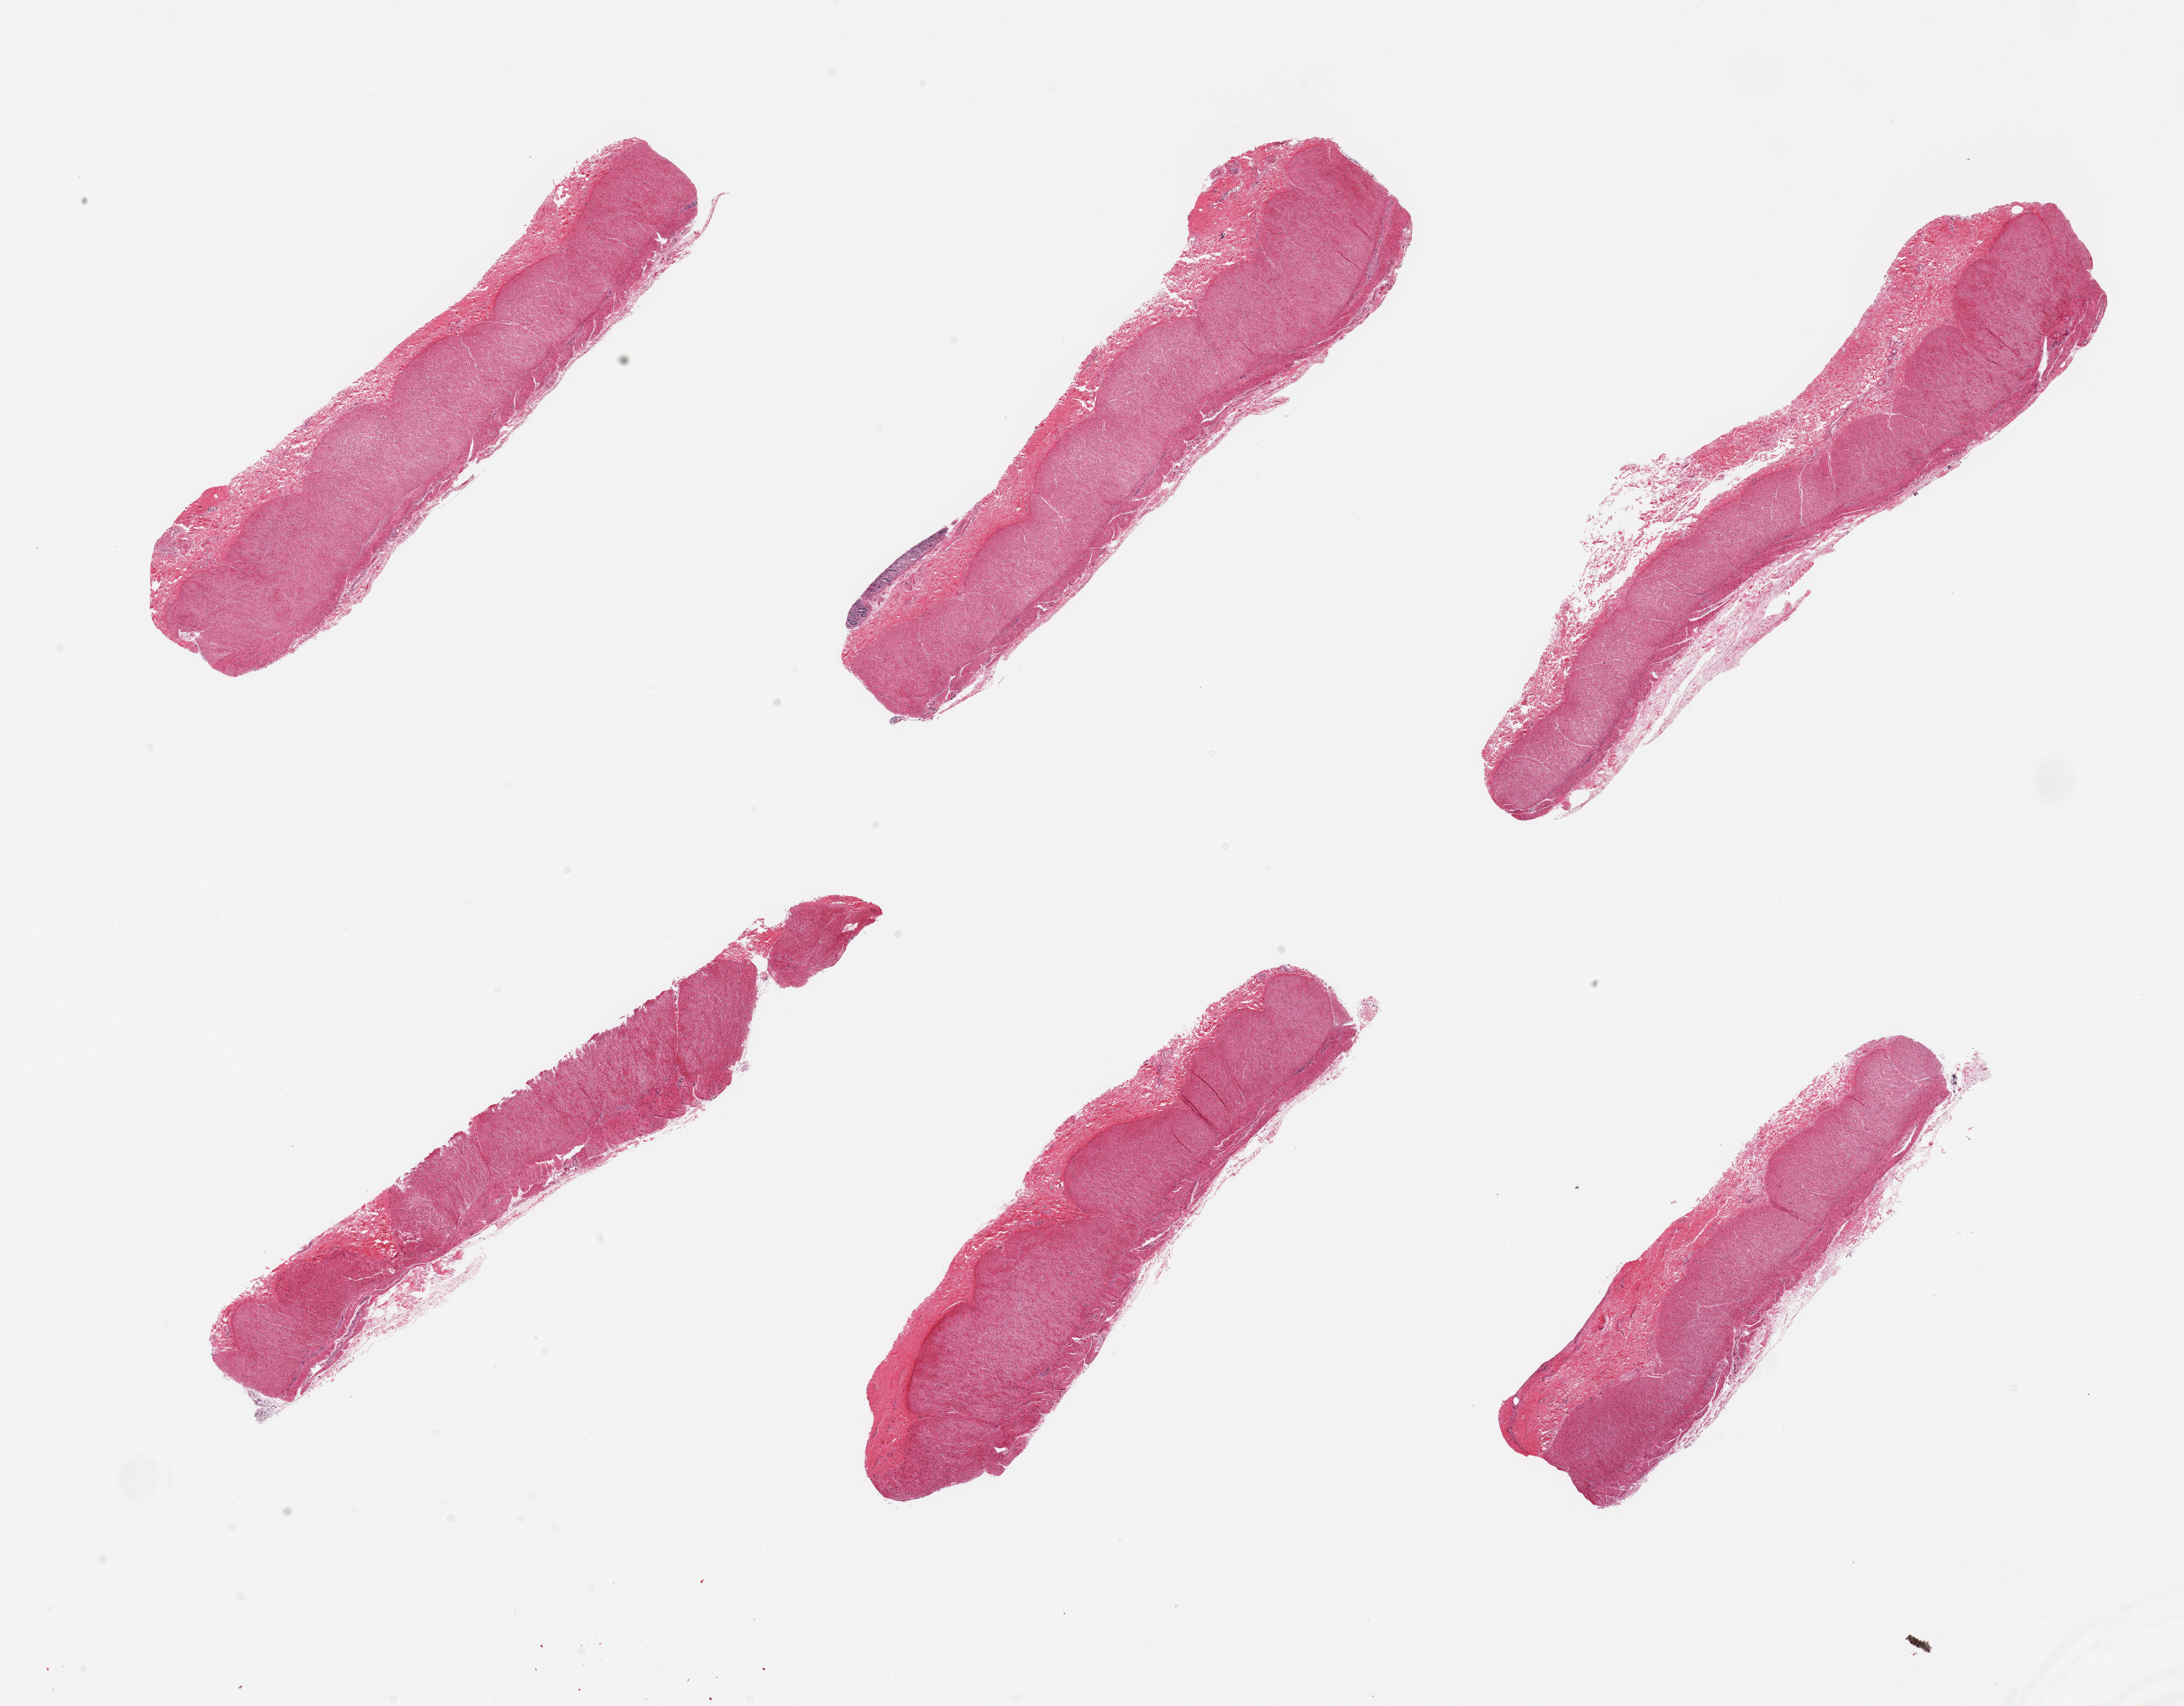
H&E whole-slide image, whole scanned area (about 25.6 x 20.0 mm, acquisition: 20x scan) shown as a low-resolution overview, PAXgene-fixed paraffin-embedded (PFPE) section, sampled site (target tissue): sigmoid colon, donor tissue sample. Male donor.
Reviewer comment on this tissue sample: 6 pieces; small autolyzed mucosal remnant (1.6 x 0.2 mm) on 1 piece.